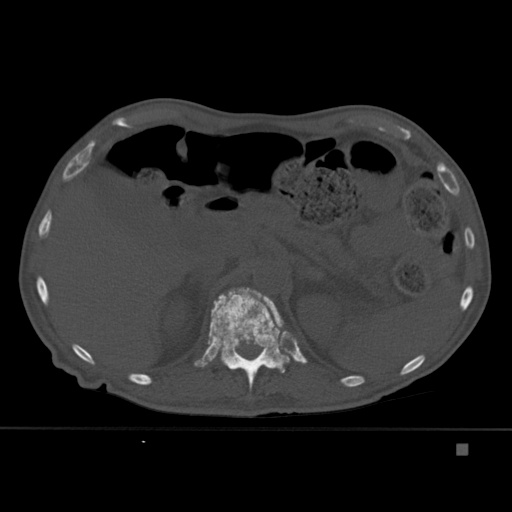
CT including the spine, one axial slice. Slice 200 of 451 in the series (ordered by position). Bone window (W 1800 / L 400 HU). 1.5 mm slice thickness. 512 × 512 image matrix, field of view 378 × 378 mm. Male patient, age 75 years. Case-level facts recorded for this patient, not image findings: primary cancer: prostate.
Annotated regions visible in this slice (semi-automatically segmented with operator editing):
- T12 vertebra: bounding box (x1, y1, x2, y2) in pixels: (208, 287, 290, 392)